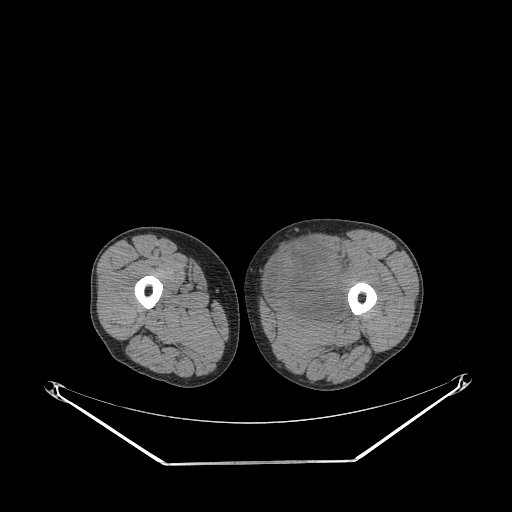
CT of an extremity soft-tissue mass (from a PET/CT study), one axial slice; position 238 of 267 along the scan axis; reconstruction kernel STANDARD; soft-tissue window (W 400 / L 40 HU); 3.75 mm slice thickness; 512 × 512 image matrix. Male patient. From the clinical record (not read from this slice): histological type: pleiomorphic liposarcoma; grade: high; site of the primary tumour: left thigh.
Annotated regions visible in this slice (expert contour drawn on MRI and transferred to this co-registered scan by the dataset authors):
- gross tumour volume including surrounding oedema: bounding box <267,240,353,321> (left, top, right, bottom; pixels)
- gross tumour volume (mass): <269,240,346,320>